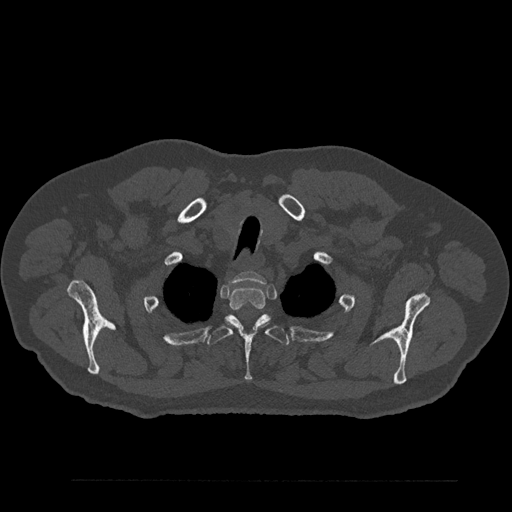
CT including the spine, one axial slice. Position 705 of 797 along the scan axis. Reconstruction kernel Br40s/3. 120 kVp. Bone window (W 1800 / L 400 HU). 0.5 mm slice thickness. 512 × 512 image matrix, field of view 430 × 430 mm. Male patient, age 61 years. From the clinical record (not read from this slice): primary cancer: prostate.
Annotated regions visible in this slice (semi-automatic segmentation, software-assisted and operator-edited):
- T1 vertebra: bounding box [x1, y1, x2, y2] px = [230, 271, 266, 284]
- T2 vertebra: [229, 286, 265, 310]
- T3 vertebra: [207, 314, 289, 381]